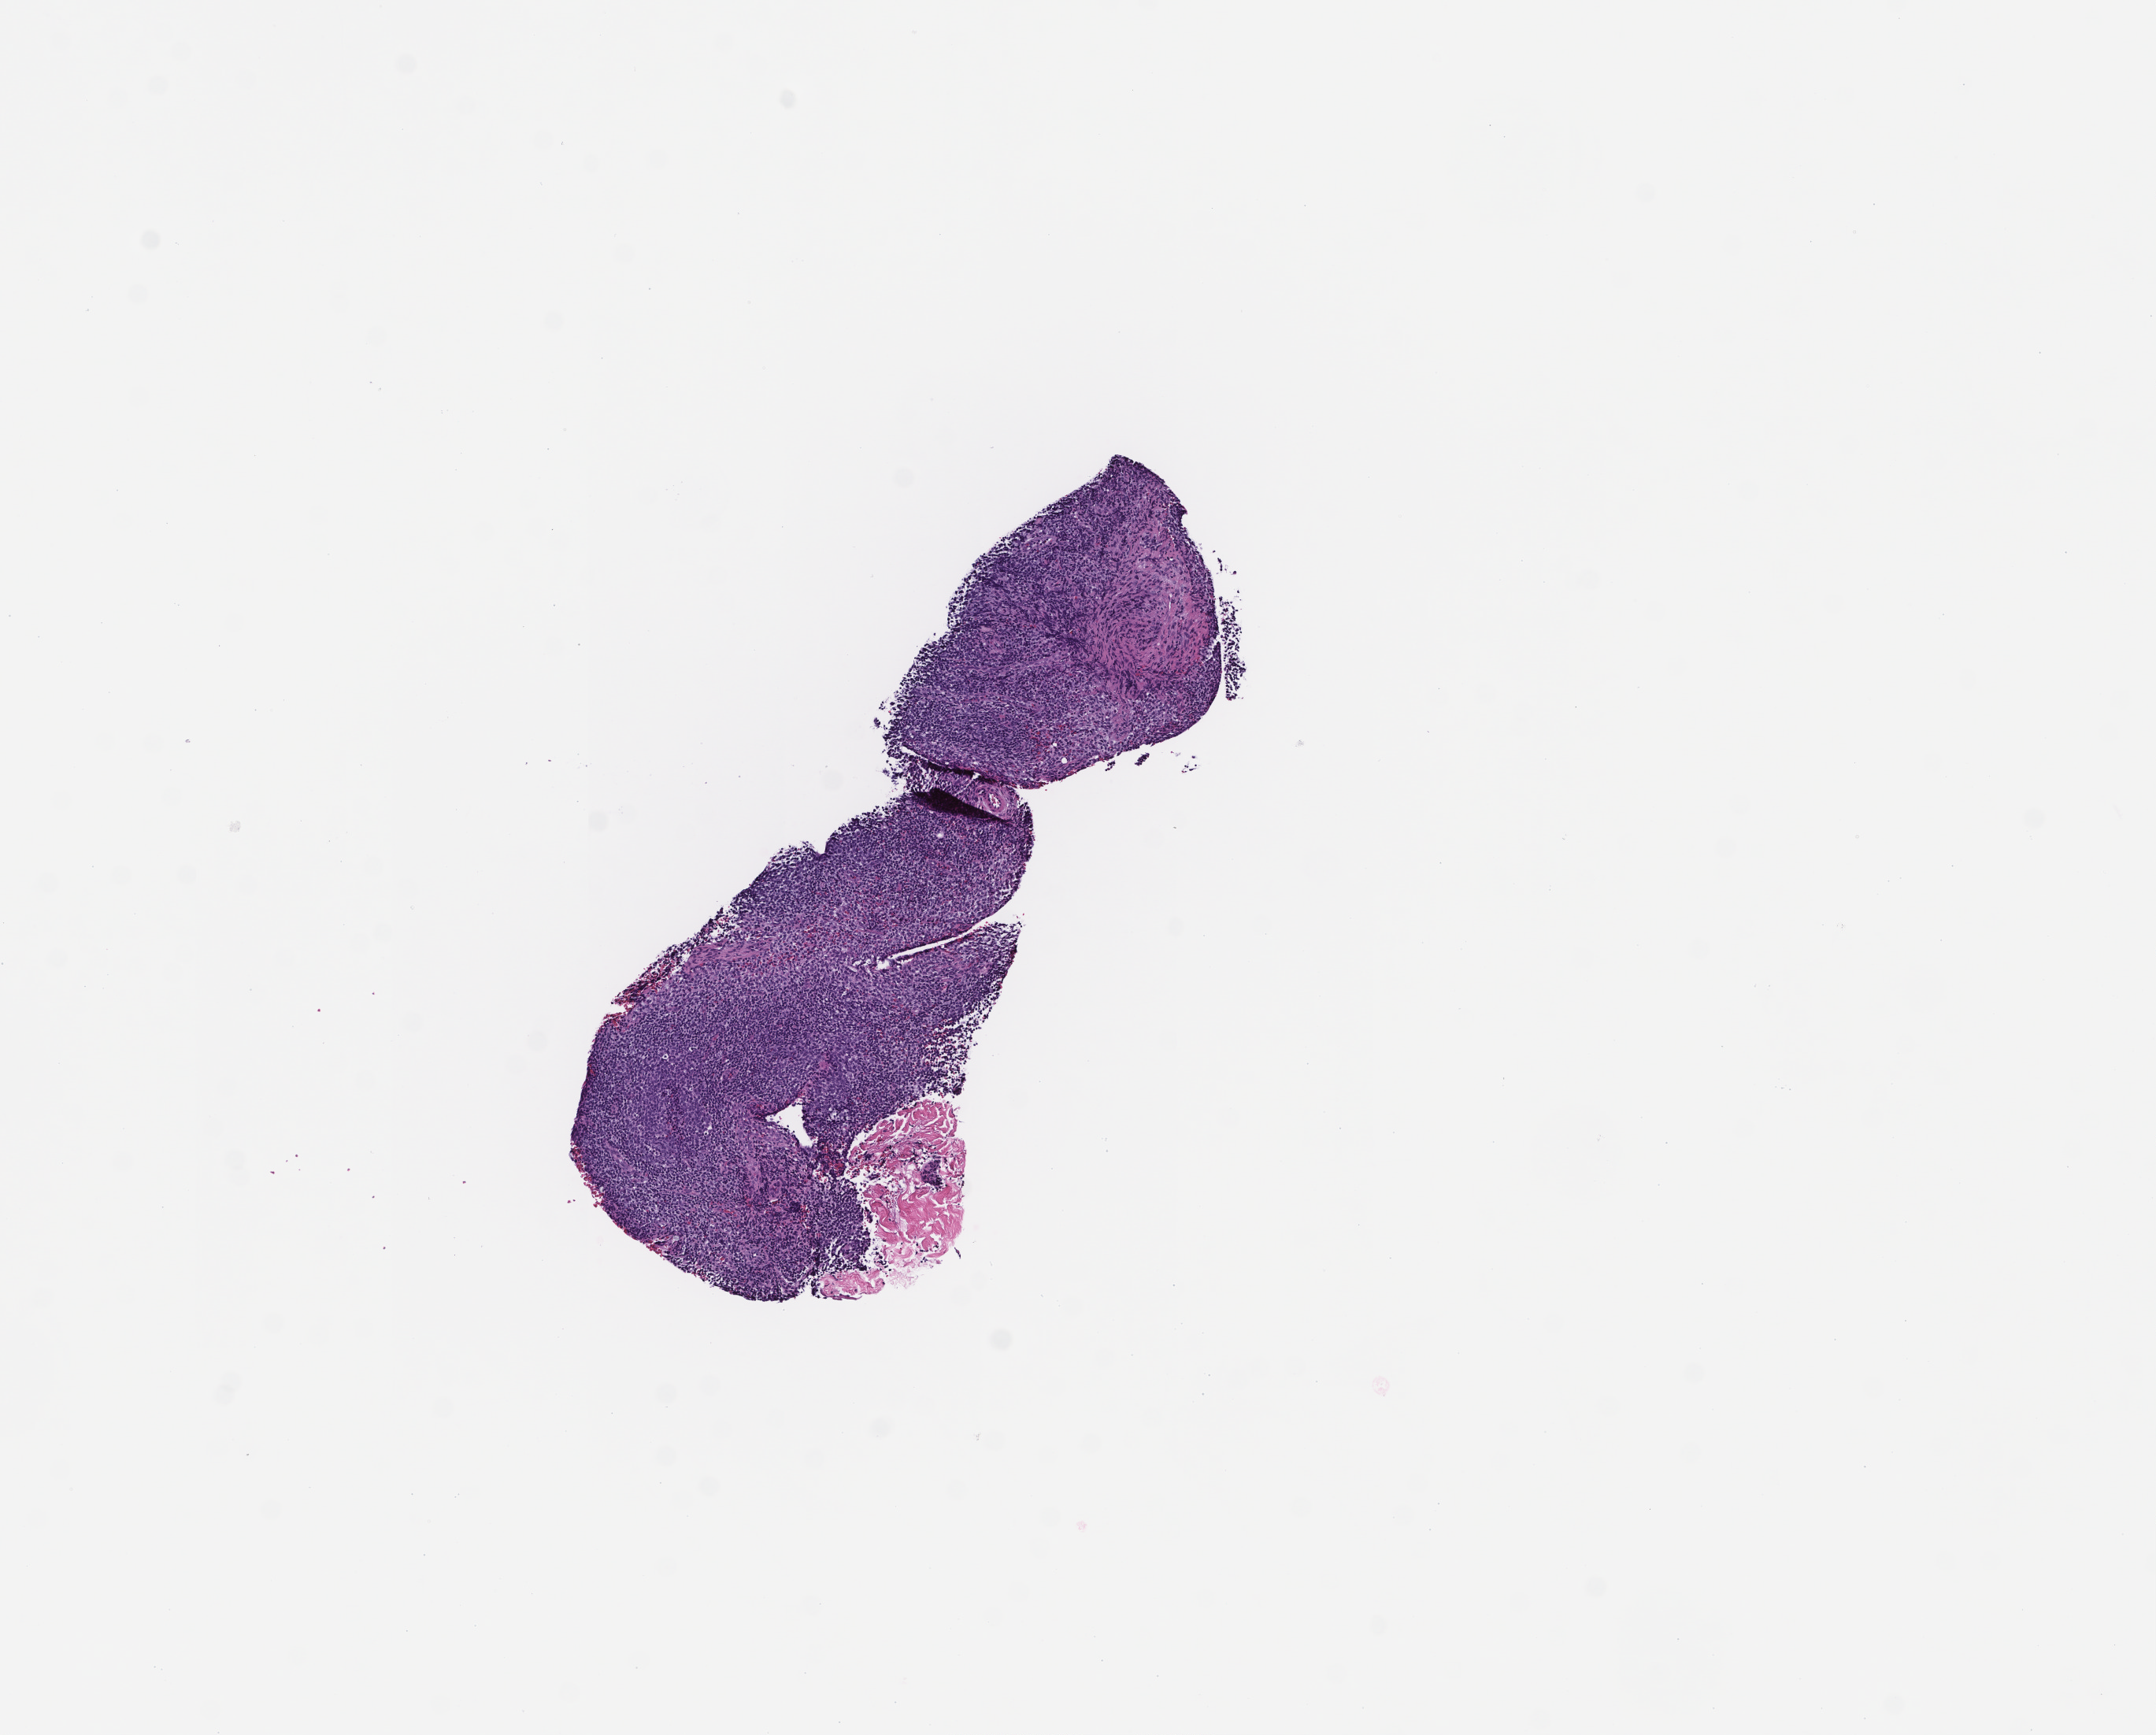
Digitized haematoxylin and eosin-stained section, a low-resolution overview of the entire scanned area, about 5.5 x 4.4 mm. Formalin-fixed paraffin-embedded section. Patient sex: male.
This section: metastasis (sampled organ not recorded). Primary diagnosis of the patient: Melanoma.